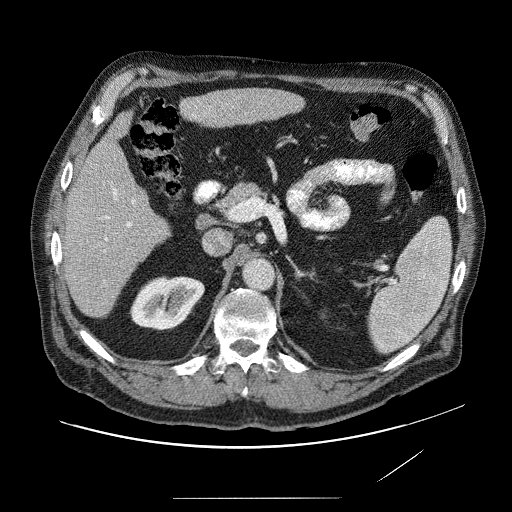
Contrast-enhanced abdominal CT (liver protocol), one axial slice; position 35 of 89 along the scan axis; reconstruction kernel STANDARD; soft-tissue window (W 400 / L 40 HU); 512 × 512 image matrix, field of view 420 × 420 mm. Case-level facts recorded for this patient, not image findings: diagnosis: hepatocellular carcinoma (patient treated with transarterial chemoembolisation; whether this scan precedes or follows treatment is not stated here); TNM stage (as recorded): Stage-IVA; Child-Pugh class: A; tumour differentiation: moderately differentiated; tumour nodularity: multinodular.
Annotated regions visible in this slice (semi-automatically segmented with operator editing):
- liver parenchyma outside the tumour (the mass and vessels are separate outlines, so this box may not span the whole liver): bounding box (x1, y1, x2, y2) in pixels: (60, 86, 310, 320)
- mass: (181, 97, 209, 128)
- liver vessels: (85, 104, 231, 281)